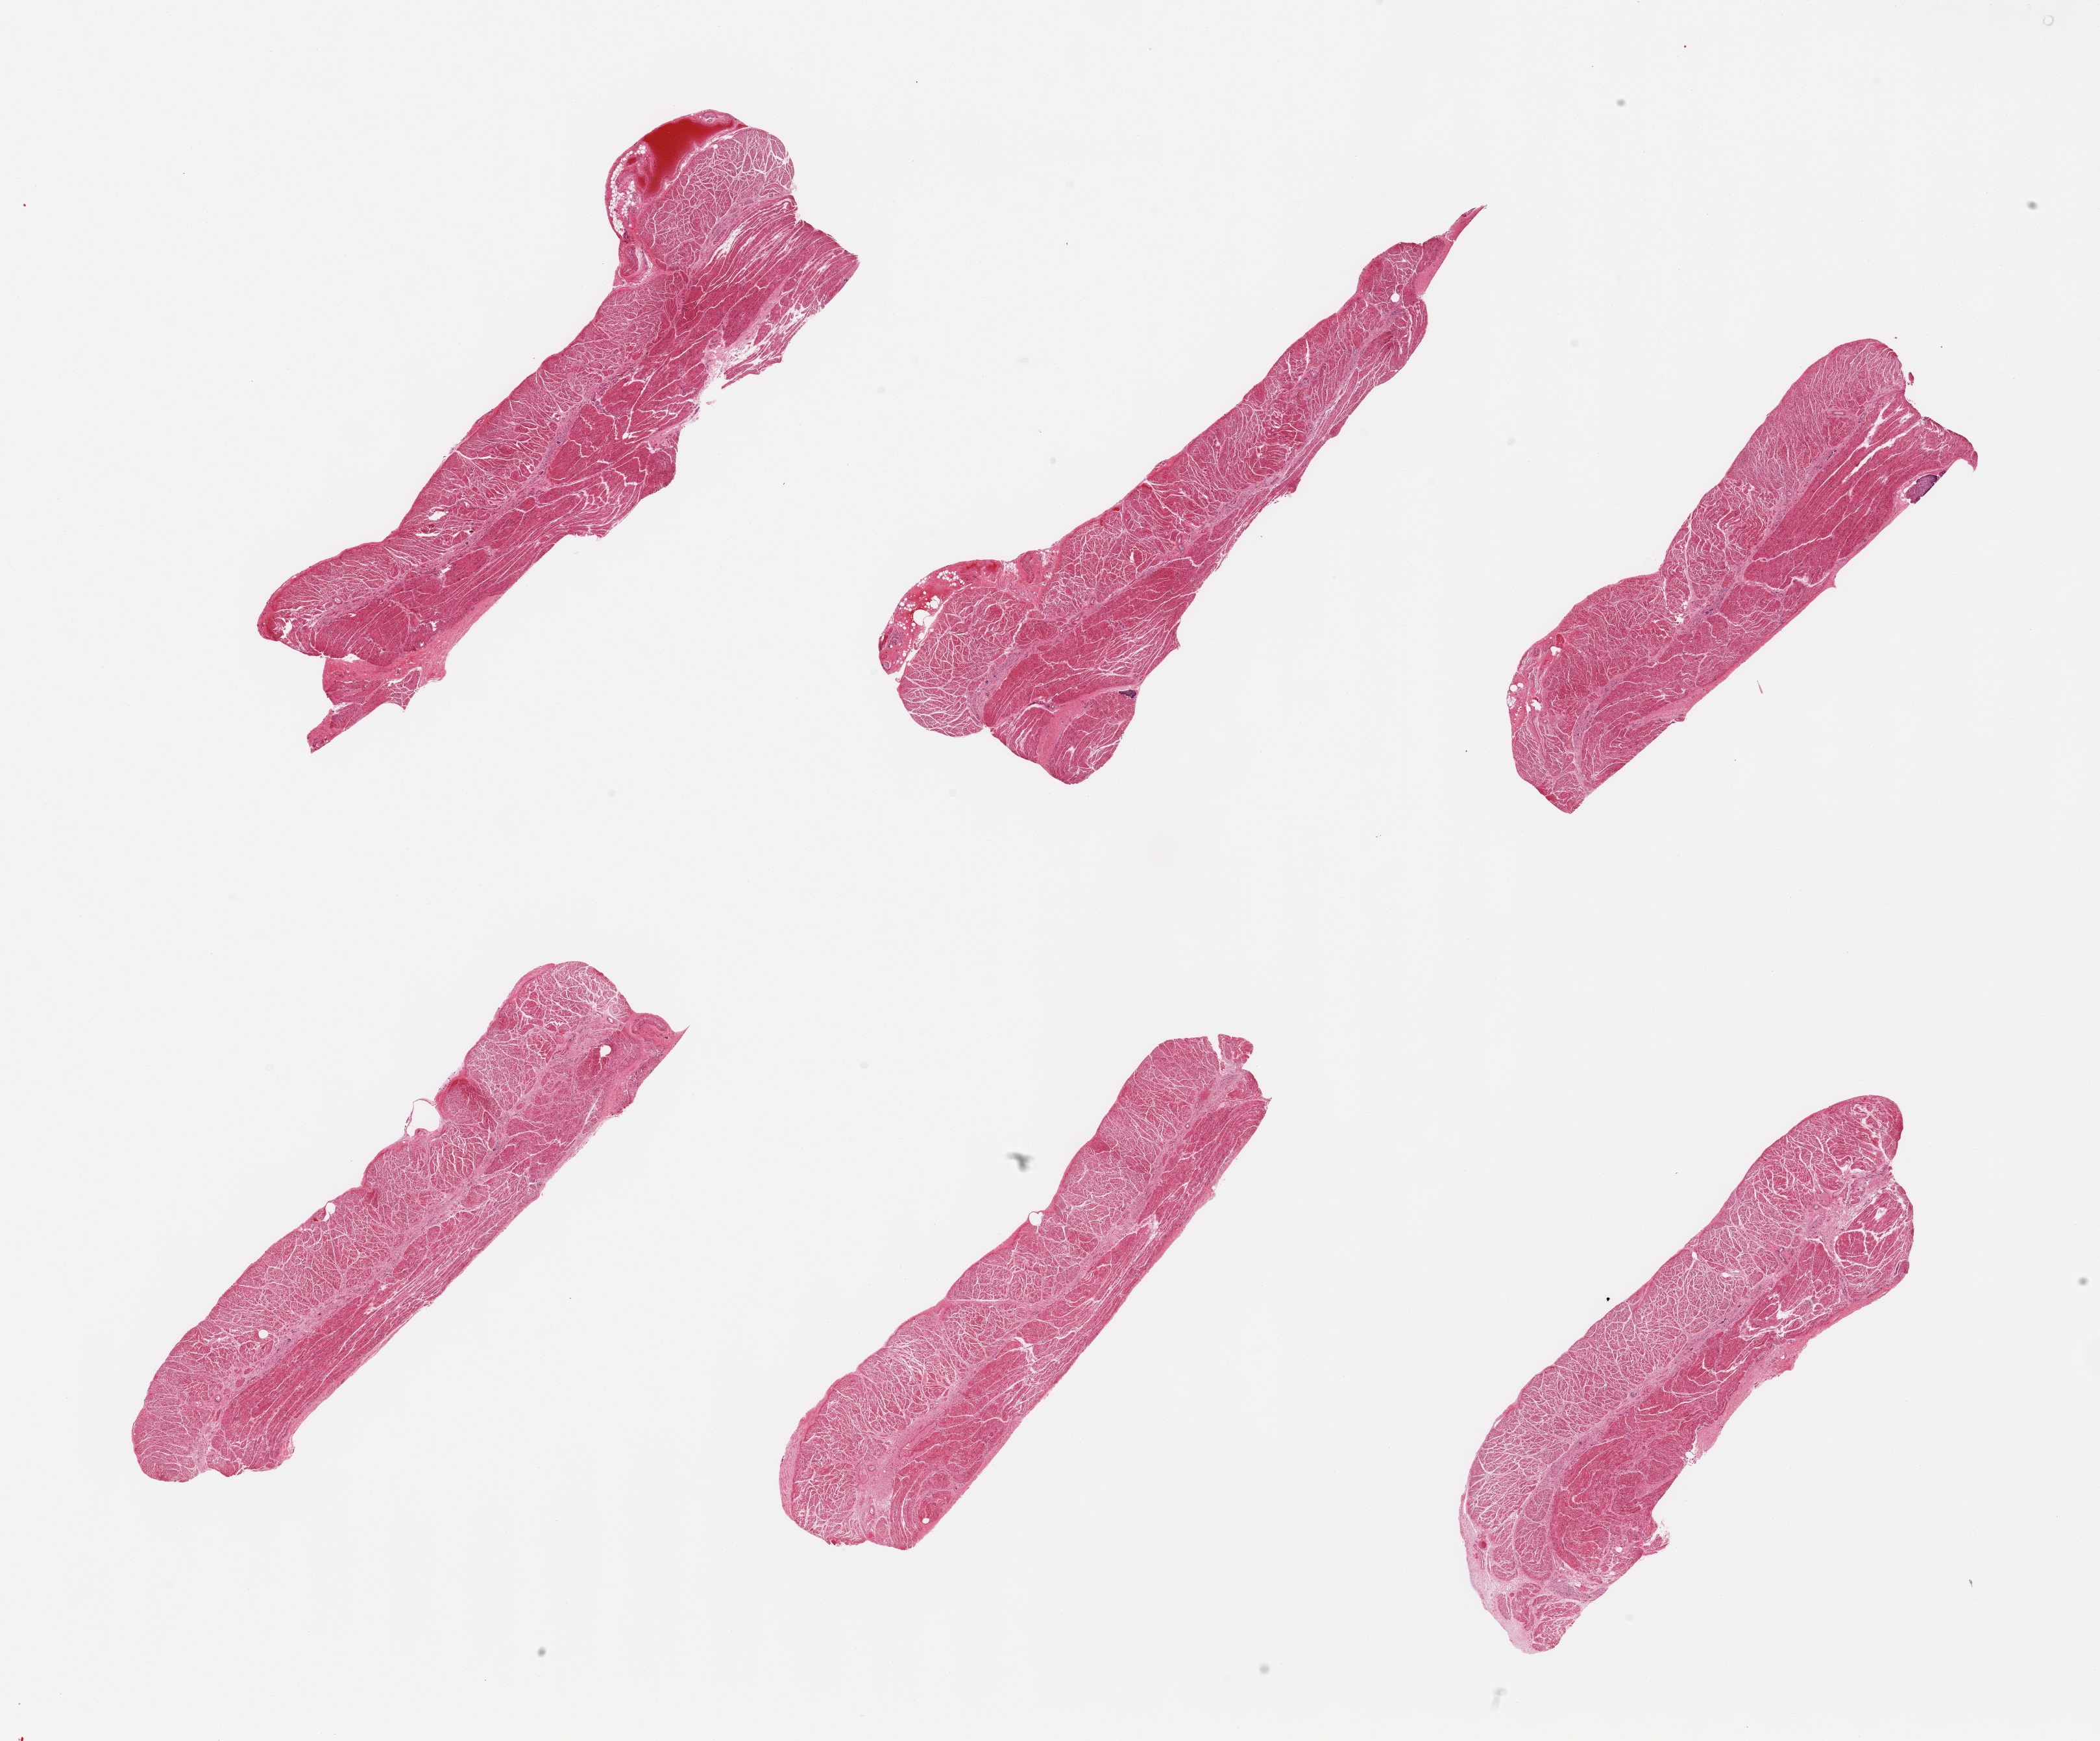
H&E whole-slide image, brightfield — whole scanned area (about 25.6 x 21.2 mm) shown as a low-resolution overview, PAXgene-fixed paraffin-embedded (PFPE) section, section of esophageal muscle (target tissue), tissue donor sample. Donor sex: male.
* reviewer comment on this tissue sample: 6 pieces, confirmed target muscularis